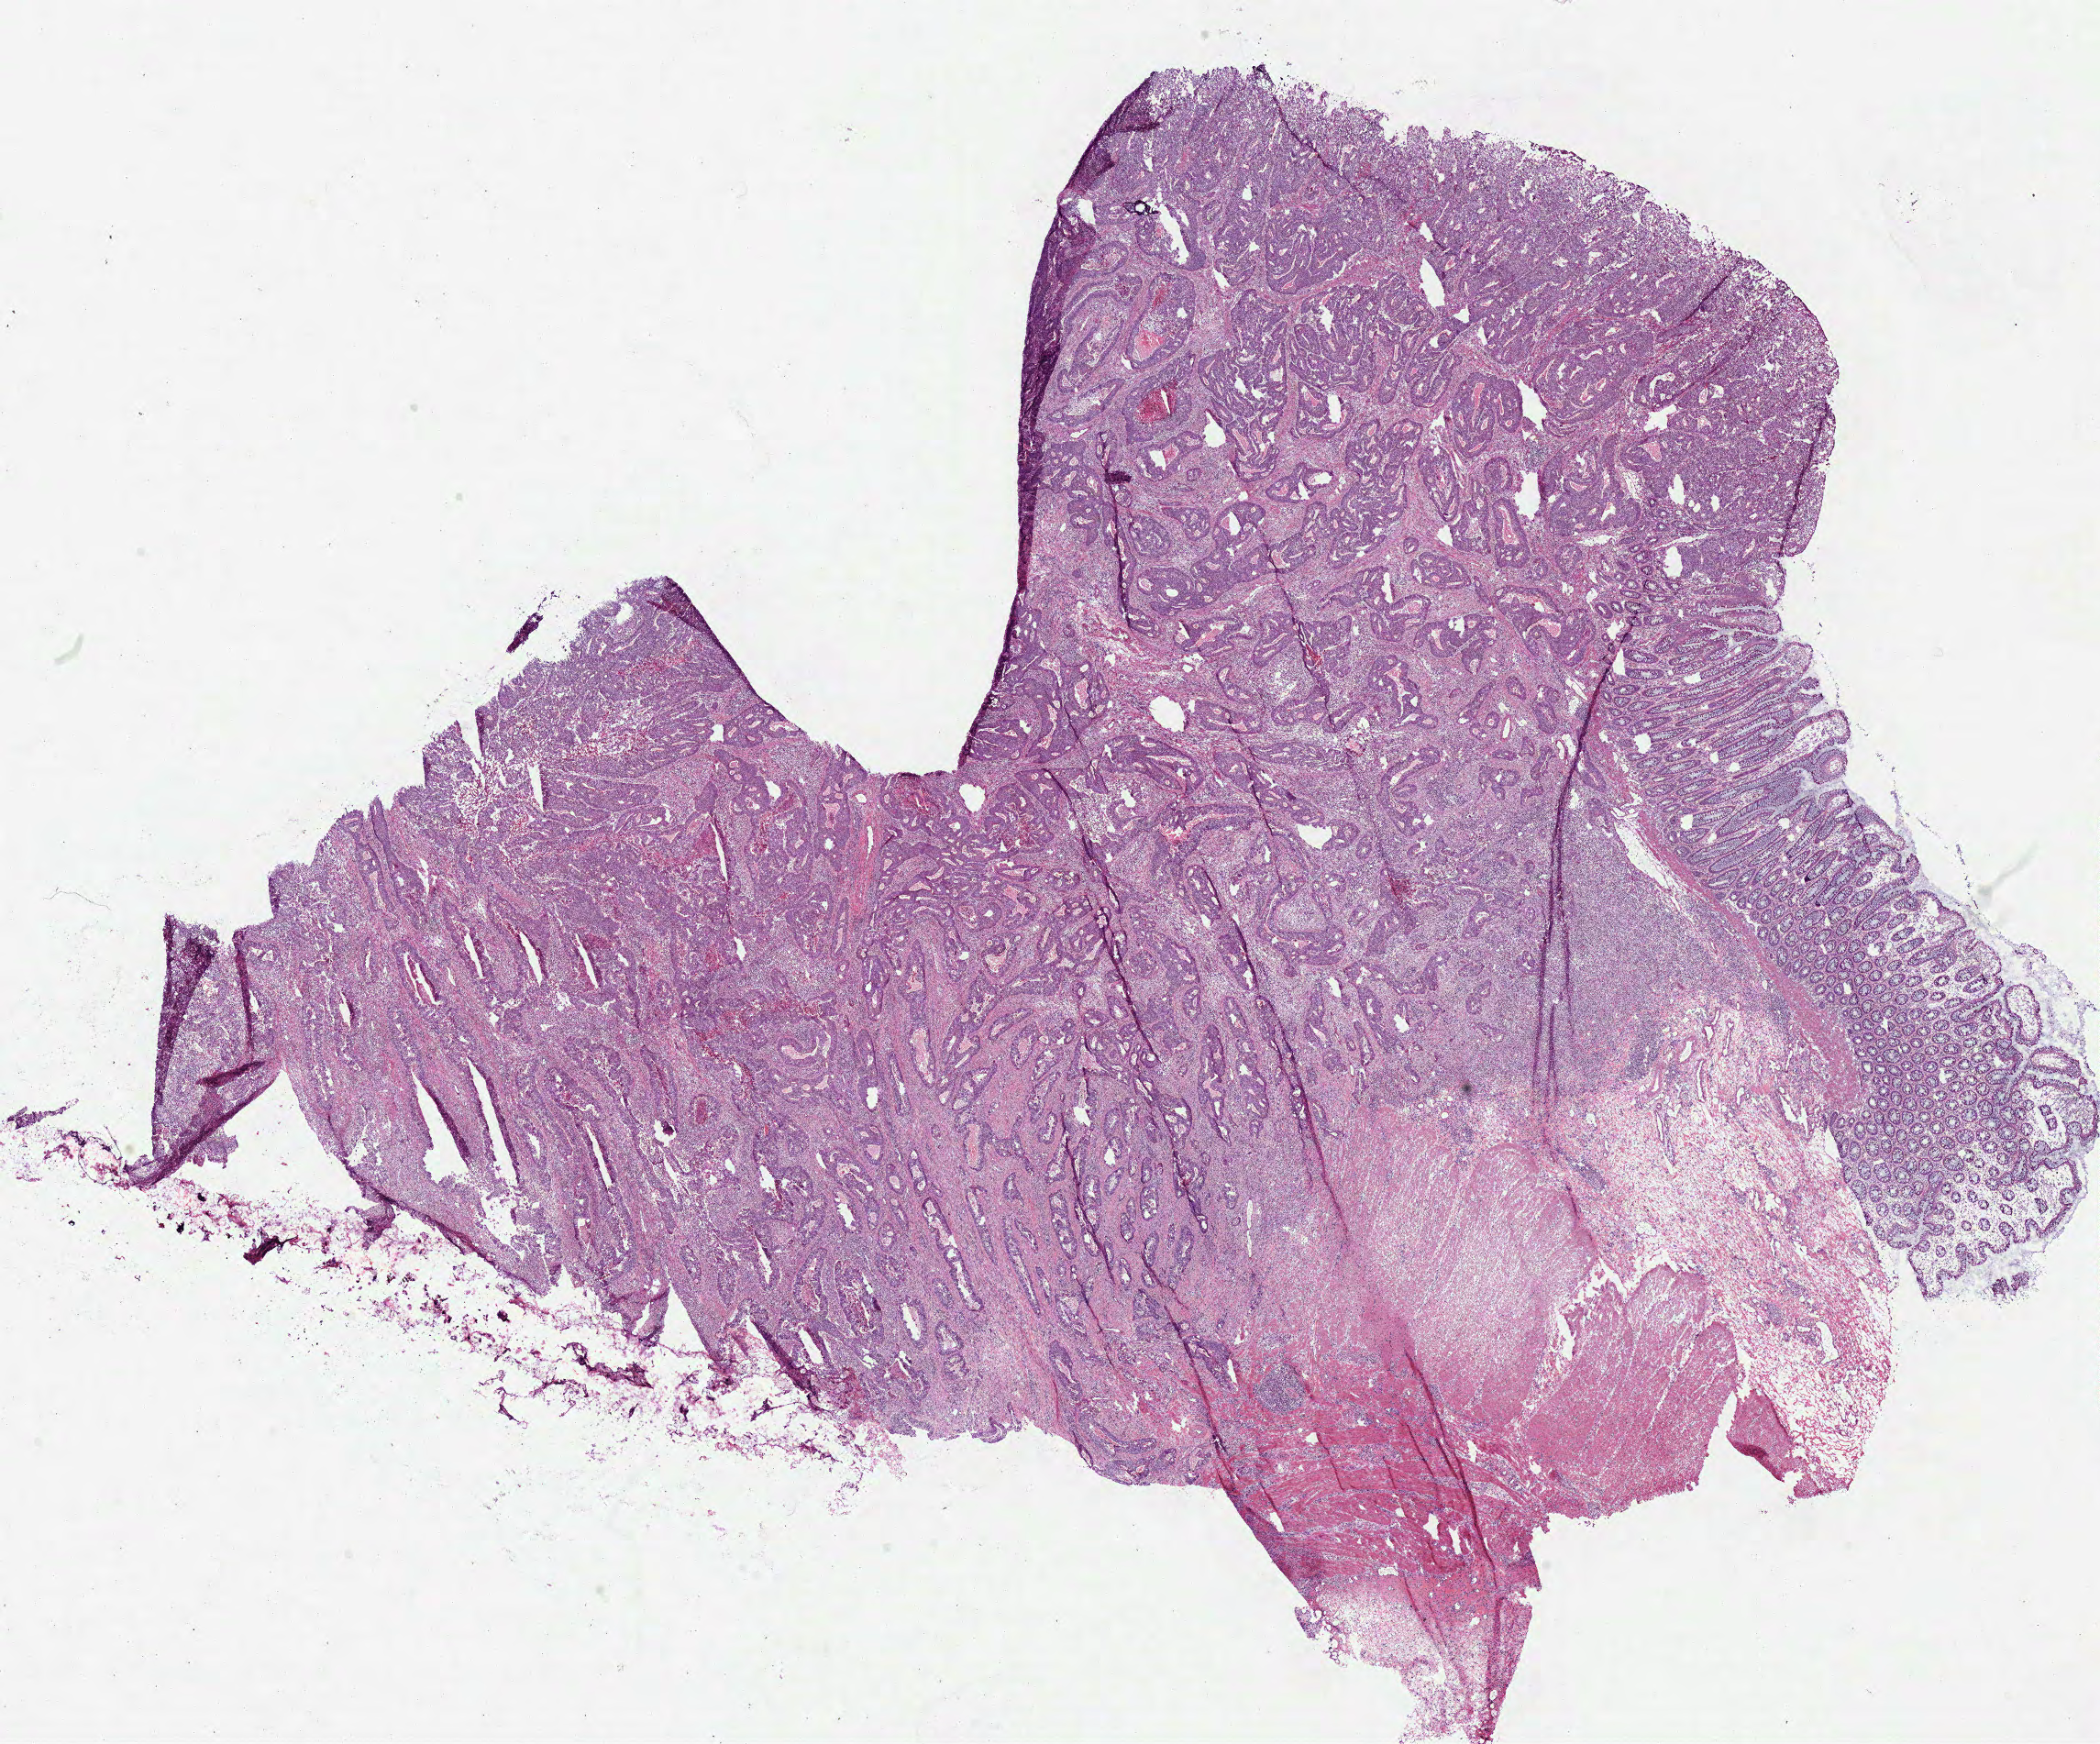
H&E-stained whole-slide image — shown as a low-resolution overview of the whole scanned area (about 18.0 x 15.0 mm). Frozen section from the bottom of the tissue portion. Primary tumour sample from the rectum. Female, age 64 years at initial diagnosis. Composition of this section per pathologist review: tumour cells 80%, tumour nuclei 80%, normal cells 15%, stromal cells 0%, necrosis 5%. Infiltration values recorded for this section: lymphocyte infiltration 10%, monocyte infiltration 0%, neutrophil infiltration 2%.
Pathologic diagnosis: Adenocarcinoma, NOS (rectosigmoid junction). Lymph nodes positive (case pathology): 0 of 12 examined. AJCC pathologic stage: IIA (7th edition).